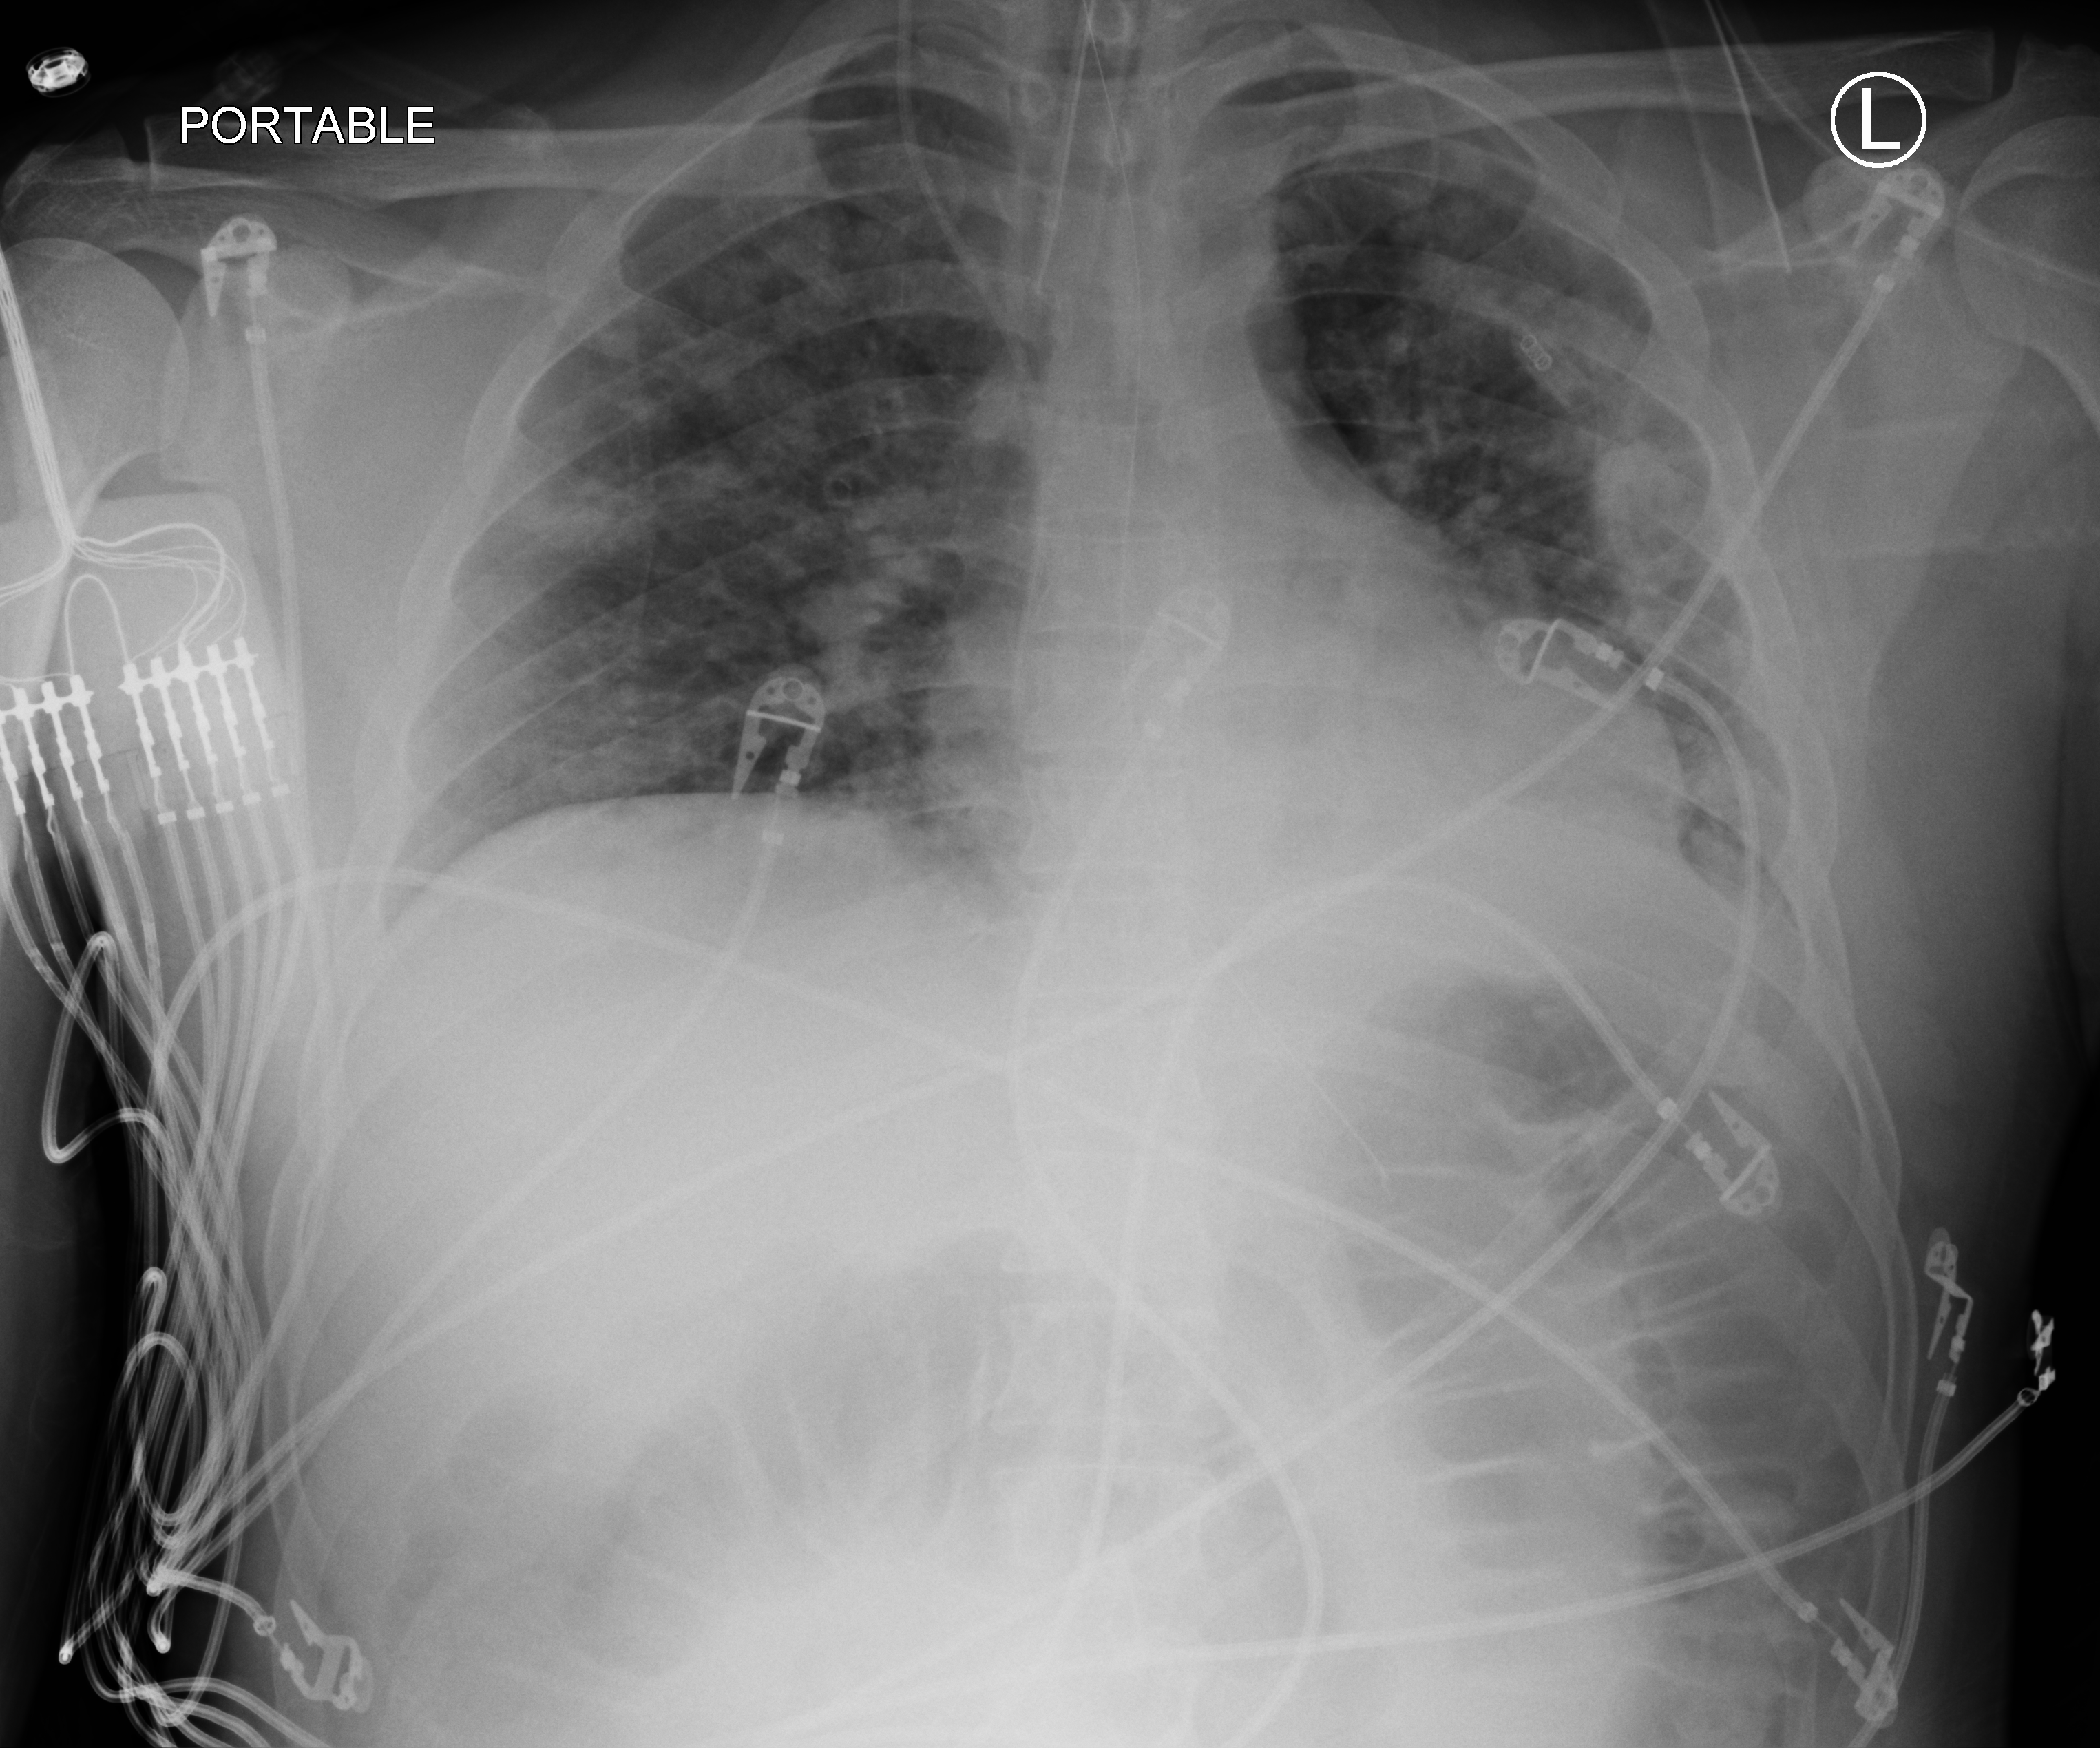
Chest X-ray (portable); anteroposterior (AP) projection. Patient hospitalised with COVID-19; male, aged 18–59 years.
Hospital-stay facts (about this admission, not read from this image; timing relative to this image not recorded):
- mechanically ventilated during this hospital stay: yes
- length of hospital stay: 20 days